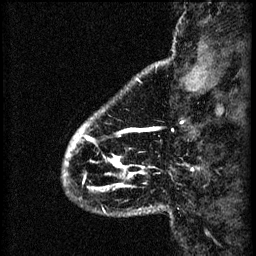
Breast MRI (dynamic contrast-enhanced), one sagittal slice. Slice 9 of 60 in the series (ordered by position). 3 images stored at this slice position (order not interpretable as contrast timing). 1.5 T. TE 4.2 ms, TR 8.2 ms. 256 × 256 image matrix, field of view 180 × 180 mm. Female patient, age 41 years.
Annotated regions visible in this slice (semi-automatic segmentation, software-assisted and operator-edited):
- analysis volume of interest (the breast-tissue region the enhancement analysis was run in; not a lesion): bounding box (x1, y1, x2, y2) in pixels: (63, 108, 150, 193)
- tumour enhancement mask (voxels above the 70 % enhancement threshold inside the analysis volume of interest): (65, 128, 150, 191)